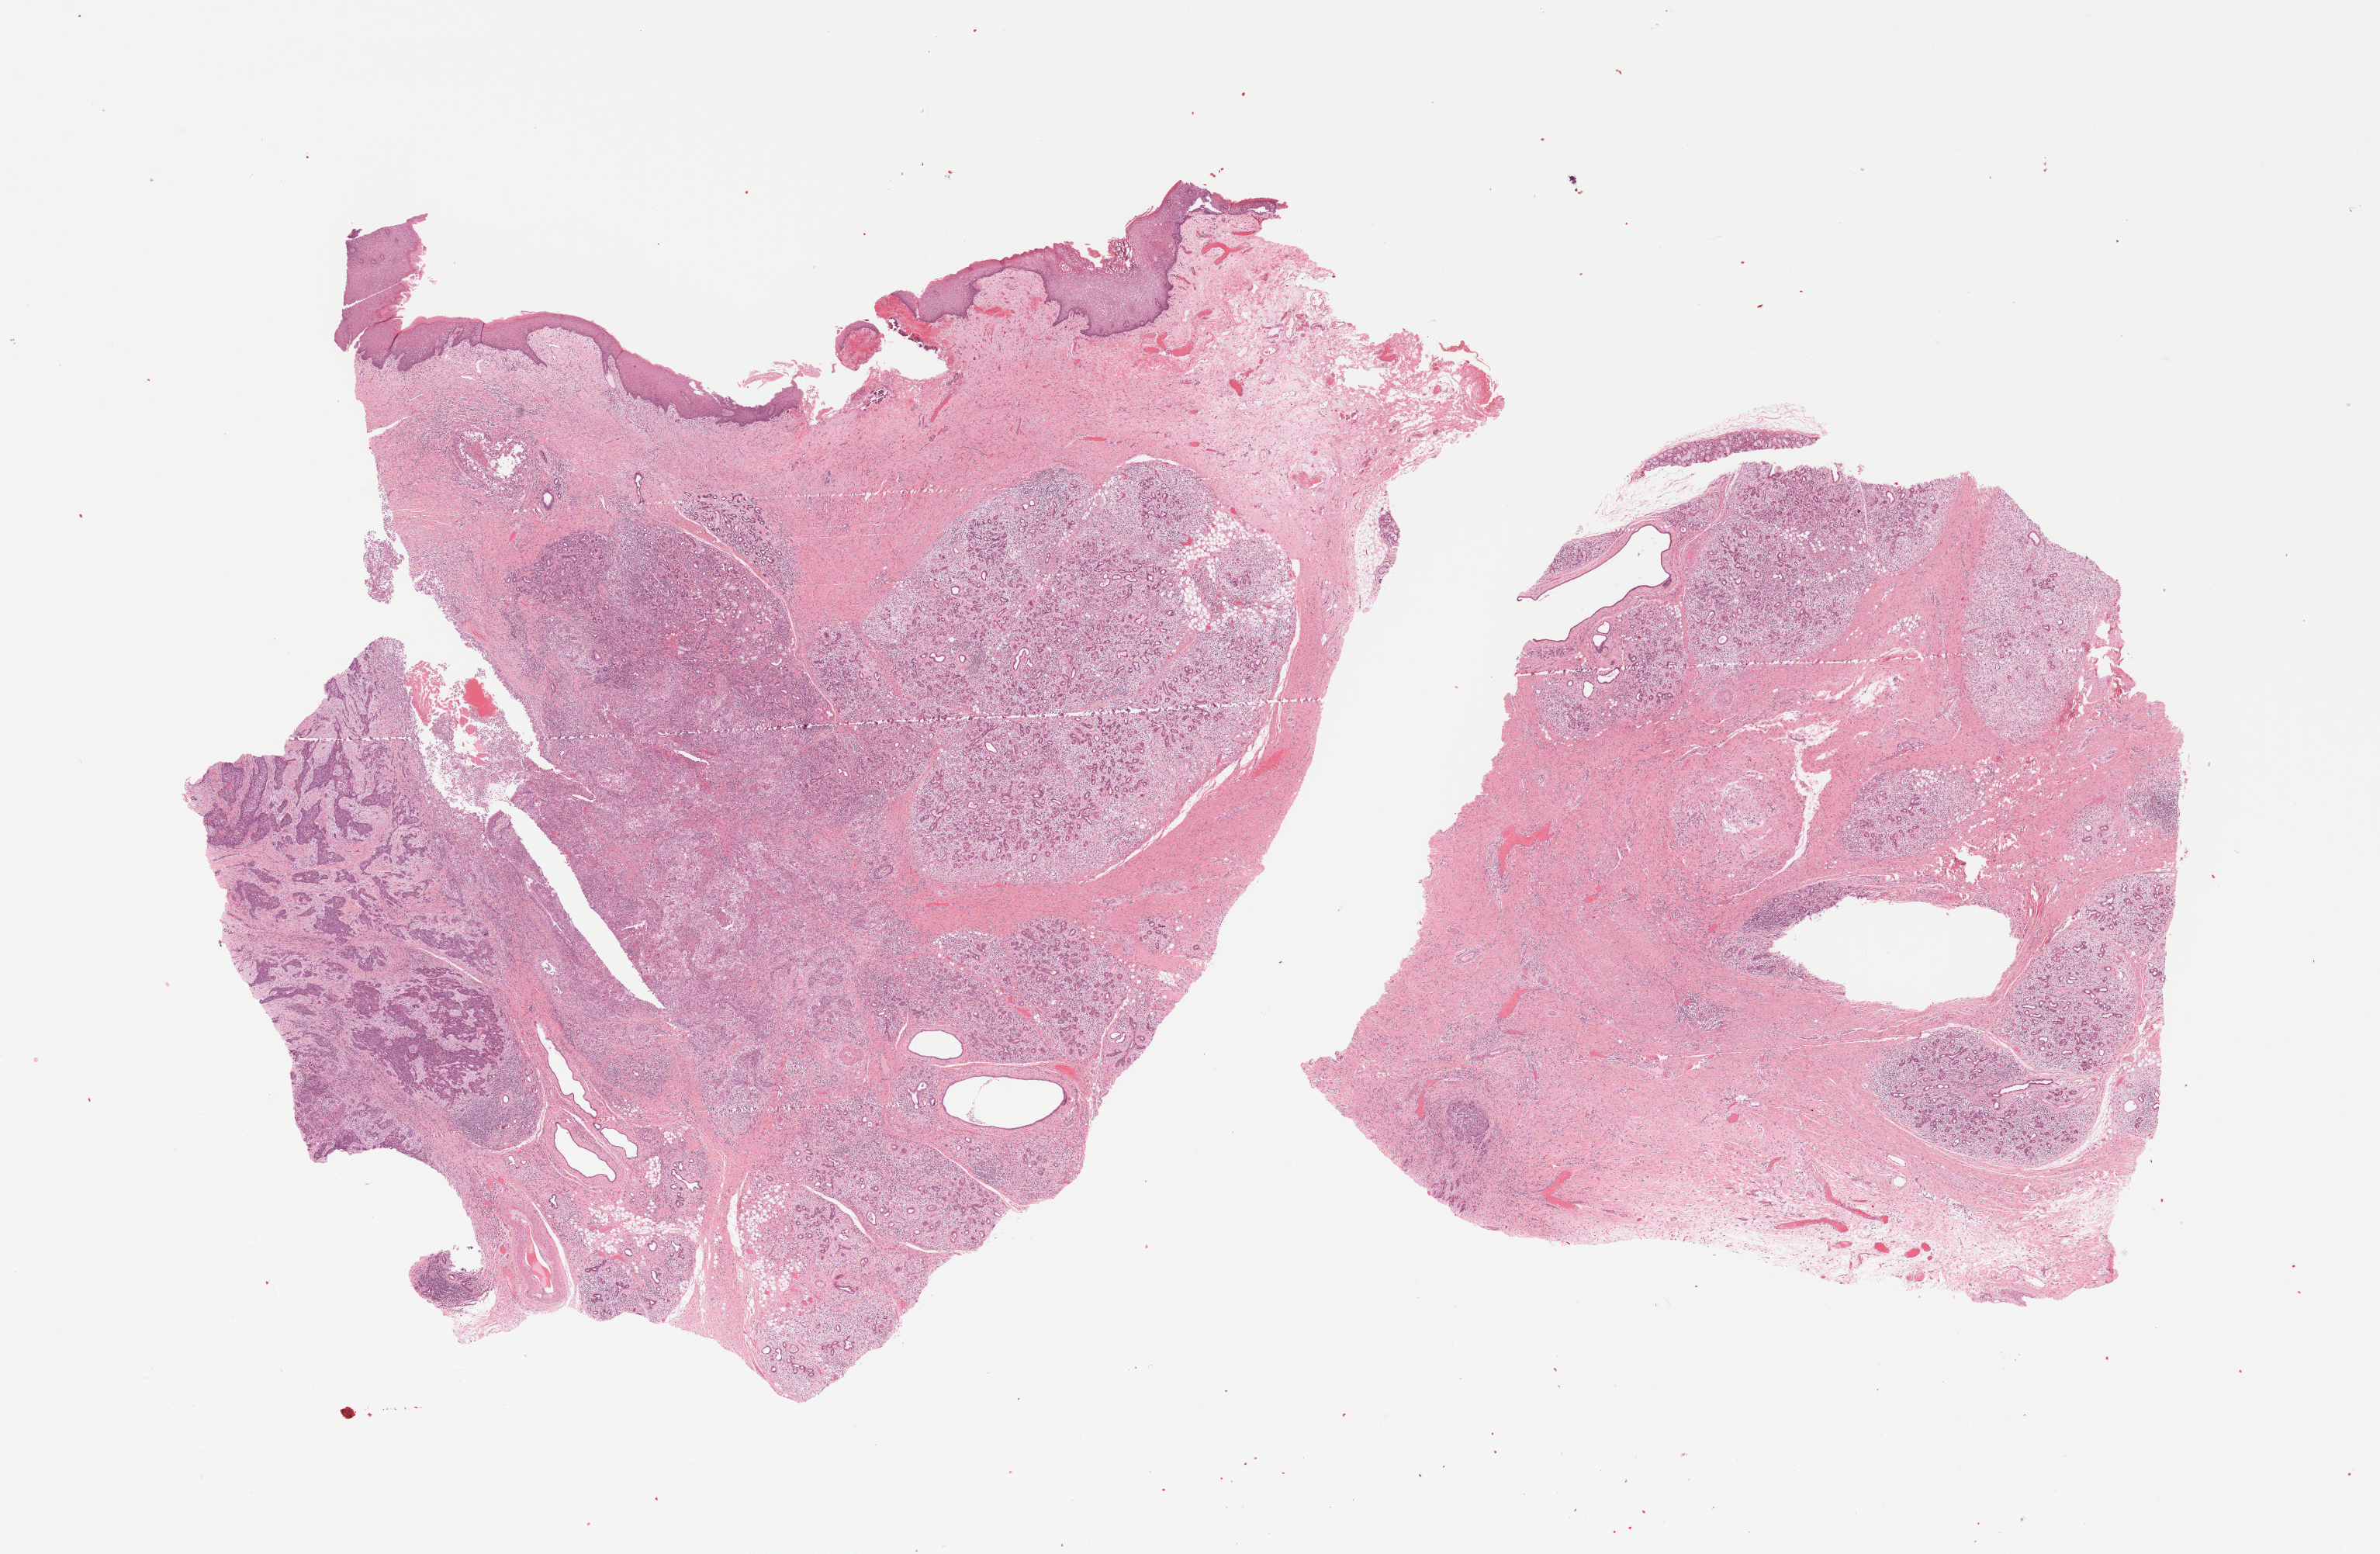
Whole-slide histology image, H&E-stained, shown as a low-resolution overview of the whole scanned area (about 24.7 x 16.1 mm). FFPE section. Head and neck, primary tumour sample. Female patient; age at initial diagnosis 71 years. Histologic grade: G2 (moderately differentiated).
Histologic diagnosis: Squamous cell carcinoma, NOS. AJCC pathologic stage: IVA (6th edition).